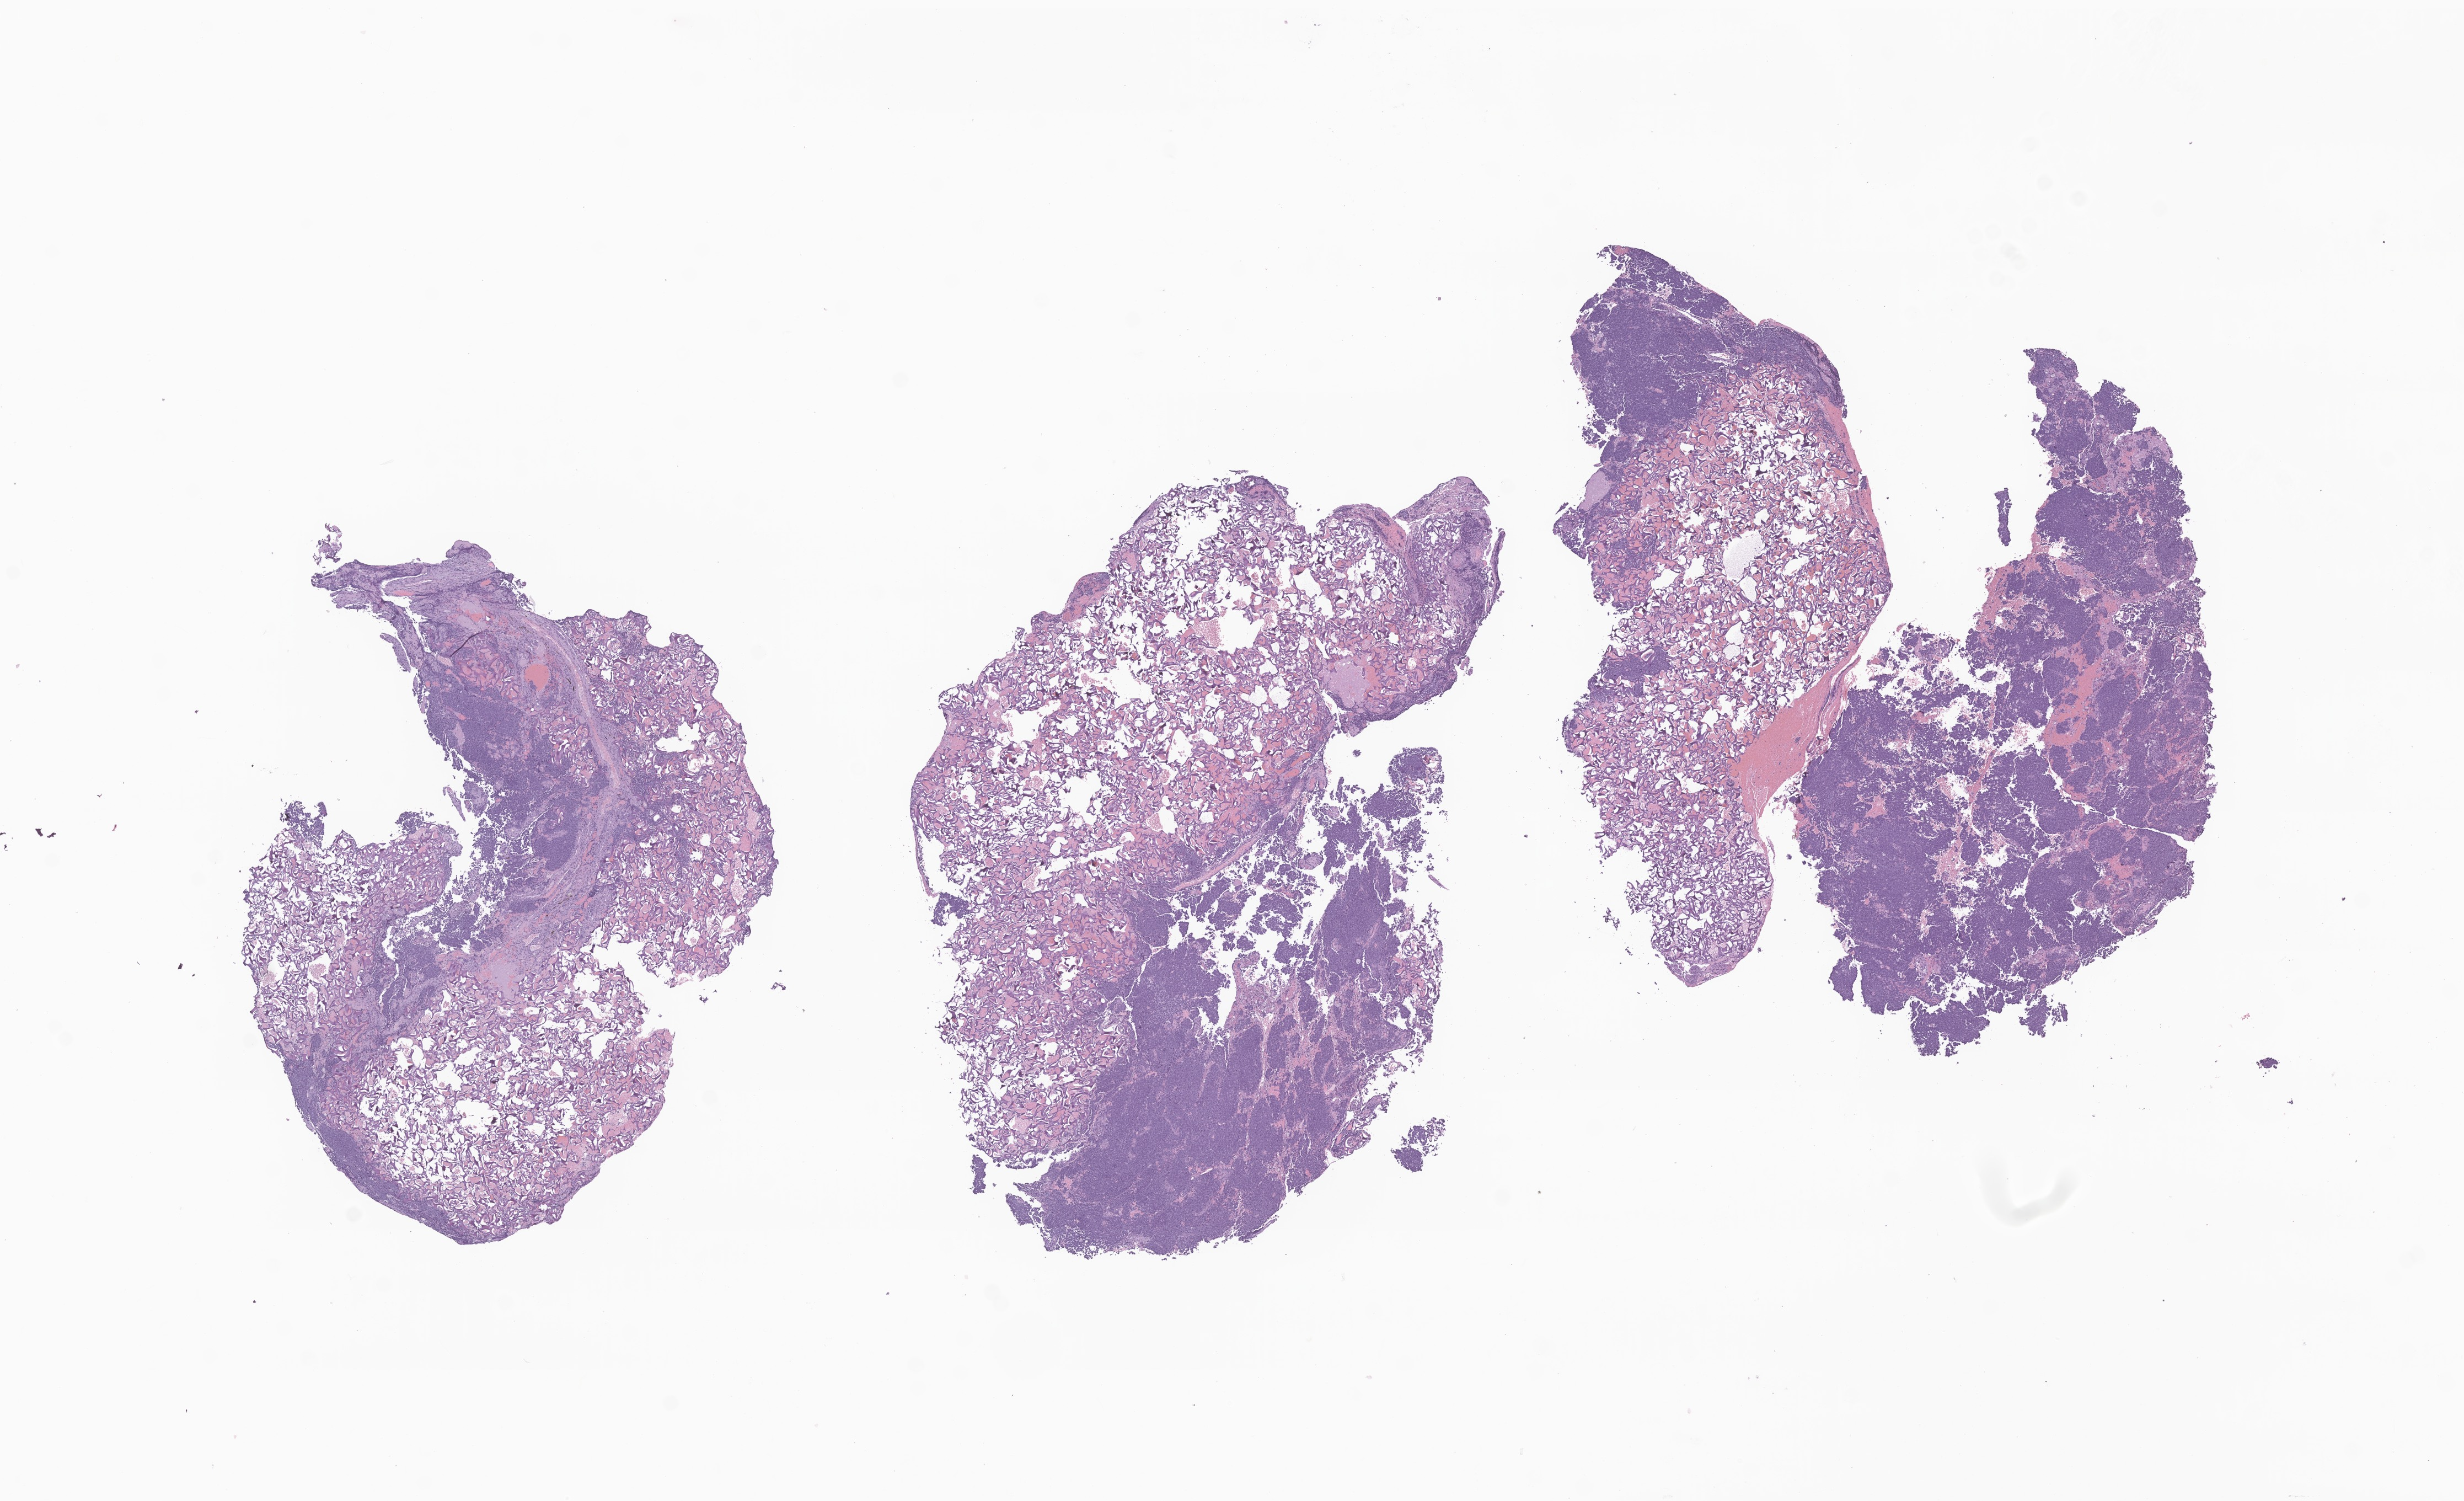
Digitized H&E-stained section of tumor tissue from the cerebellum, shown as a low-resolution overview of the whole scanned area (about 18.8 x 11.5 mm); formalin-fixed paraffin-embedded section. Patient: female, age 276 months.
Diagnosis: Medulloblastoma, NOS.